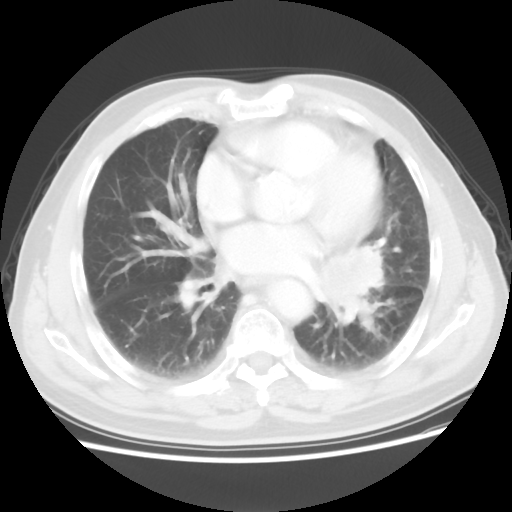
Chest CT, one axial slice; reconstruction kernel STANDARD; 120 kVp; lung window (W 1500 / L -600 HU); 512 × 512 image matrix, field of view 360 × 360 mm. Male patient, age 75 years. Case-level facts recorded for this patient, not image findings: clinical TNM (as recorded): T3 N0 M0.
Outlined on this slice (bounding box drawn by a radiologist):
- lung tumour (recorded histology: squamous cell carcinoma): bounding box [x1, y1, x2, y2] px = [316, 238, 392, 325]